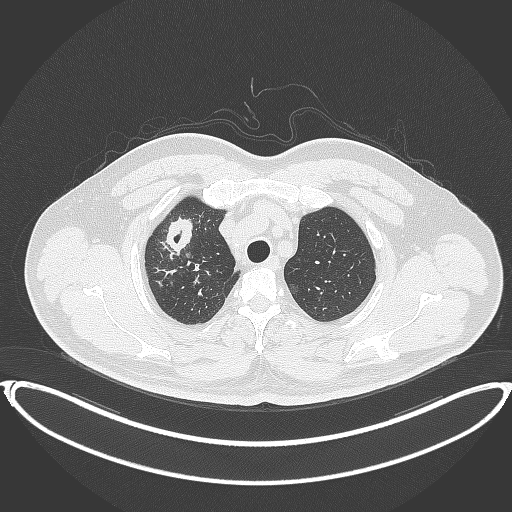
Chest CT, one axial slice; position 325 of 399 along the scan axis; reconstruction kernel B70f; 120 kVp; lung window (W 1500 / L -600 HU); 1 mm slice thickness; 512 × 512 image matrix. Male patient, age 53 years. Case-level facts recorded for this patient, not image findings: clinical TNM (as recorded): T2a N0 M0.
Outlined on this slice (bounding box drawn by a radiologist):
- lung tumour (recorded histology: adenocarcinoma): bounding box (x1, y1, x2, y2) in pixels: (168, 215, 197, 256)